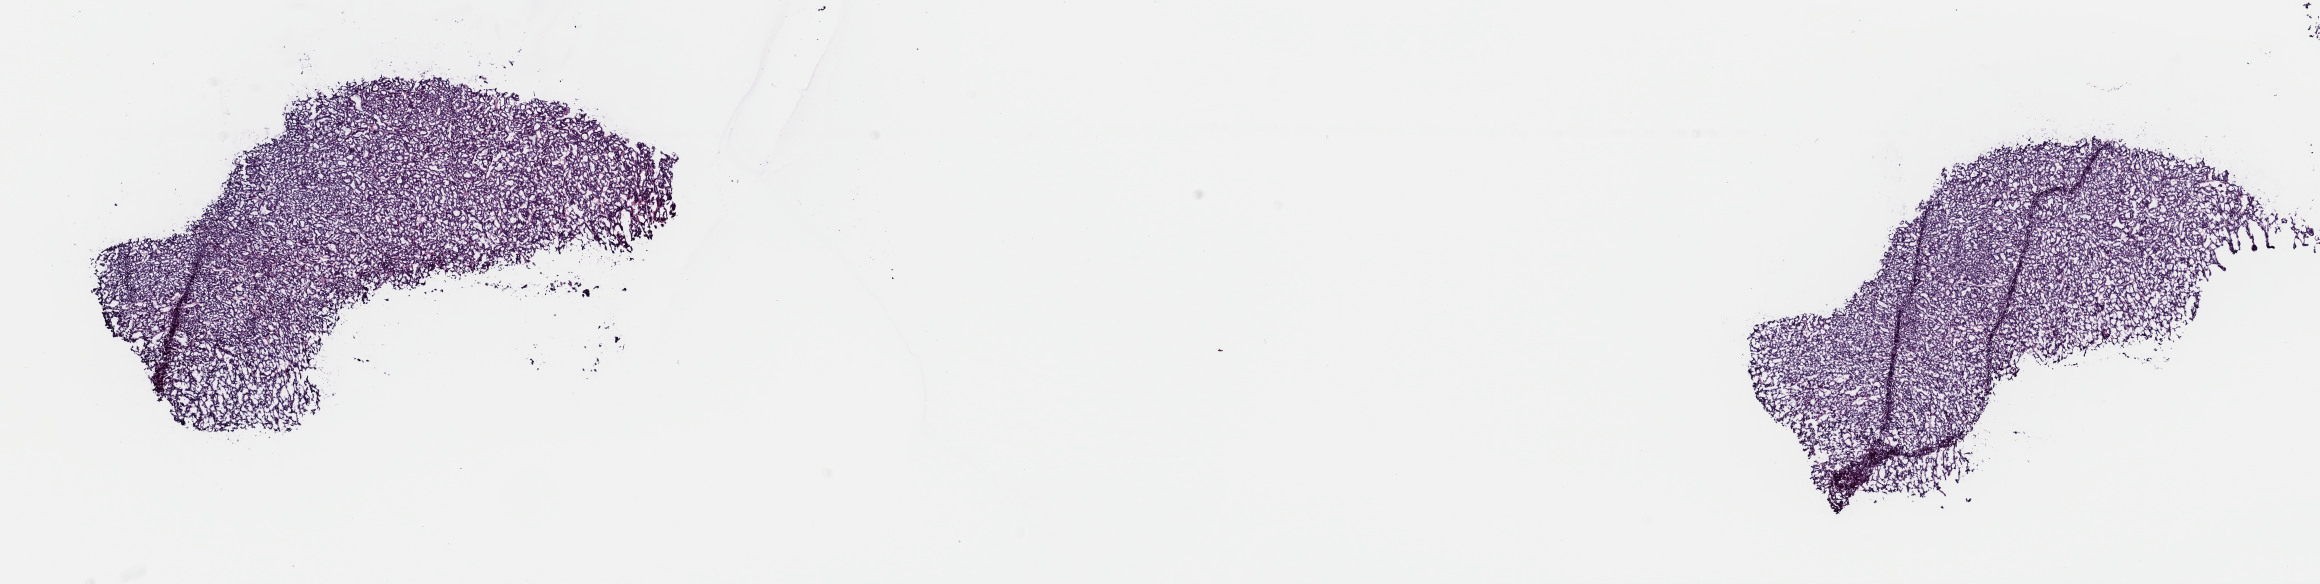
Whole-slide histology image, Hematoxylin and eosin (H&E) stained, shown as a low-resolution overview of the whole scanned area (about 18.3 x 4.6 mm, acquisition: 40x scan), frozen section from the top of the tissue portion, primary tumour sample from the thyroid. Female patient; age at initial diagnosis 62 years. Slide review estimates, as recorded: tumour cells 90%, tumour nuclei 90%, normal cells 0%, stromal cells 10%, necrosis 0%. Infiltration values recorded for this section: lymphocyte infiltration 1%, monocyte infiltration 0%, neutrophil infiltration 0%.
• AJCC pathologic stage: III (7th edition)
• laterality: right
• pathologic diagnosis: Papillary carcinoma, follicular variant (thyroid gland)